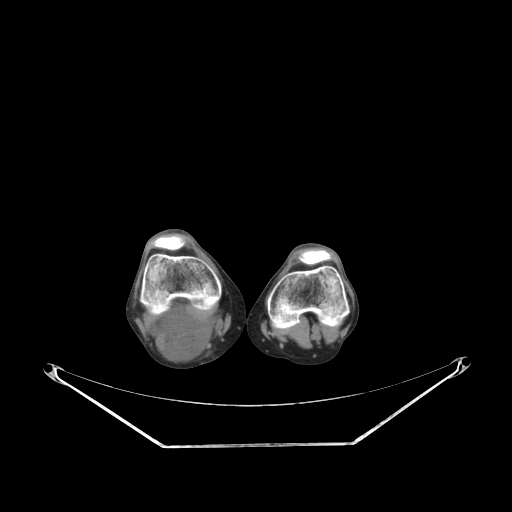
CT of an extremity soft-tissue mass (from a PET/CT study), one axial slice. Slice 170 of 267 in the series (ordered by position). Soft-tissue window (W 400 / L 40 HU). 512 × 512 image matrix, field of view 500 × 500 mm. Female patient. Case-level facts recorded for this patient, not image findings: histological type: liposarcoma; site of the primary tumour: right thigh.
Outlined on this slice (expert contour drawn on MRI and transferred to this co-registered scan by the dataset authors):
- gross tumour volume (mass): bounding box <149,301,220,362> (left, top, right, bottom; pixels)